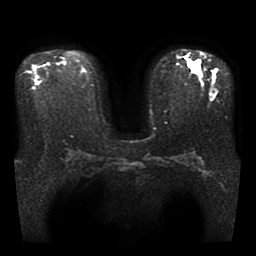
Breast MRI, one axial slice; diffusion-weighted series; image 2 of 4 stored at this slice position (different b-values; order by instance number); 1.5 T; 5 mm slice thickness; 256 × 256 image matrix, field of view 330 × 330 mm. Female patient.
Outlined on this slice (expert manual segmentation):
- tumour on diffusion-weighted imaging: bounding box (x1, y1, x2, y2) in pixels: (188, 63, 199, 74)